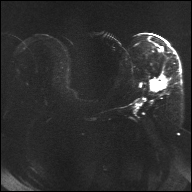
Breast MRI, one axial slice; diffusion-weighted series; image 2 of 4 stored at this slice position (different b-values; order by instance number); 1.5 T; 4 mm slice thickness; 192 × 192 image matrix, field of view 360 × 360 mm. Female patient.
Structures marked on this image (expert manual segmentation):
- tumour on diffusion-weighted imaging: box from (x=151, y=75) to (x=167, y=91) px